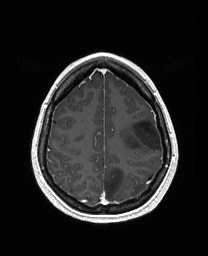
Brain MRI from a brain-tumour surgery series, one axial slice. Slice 123 of 176 in the series (ordered by position). T1-weighted post-contrast. 208 × 256 image matrix, field of view 203 × 250 mm. From the clinical record (not read from this slice): histopathology: Astrocytoma; WHO grade: 3; IDH mutation: yes; tumour location: Left Frontal.
Structures marked on this image (outlined manually by an expert reader):
- tumour: bounding box <123,117,161,152> (left, top, right, bottom; pixels)